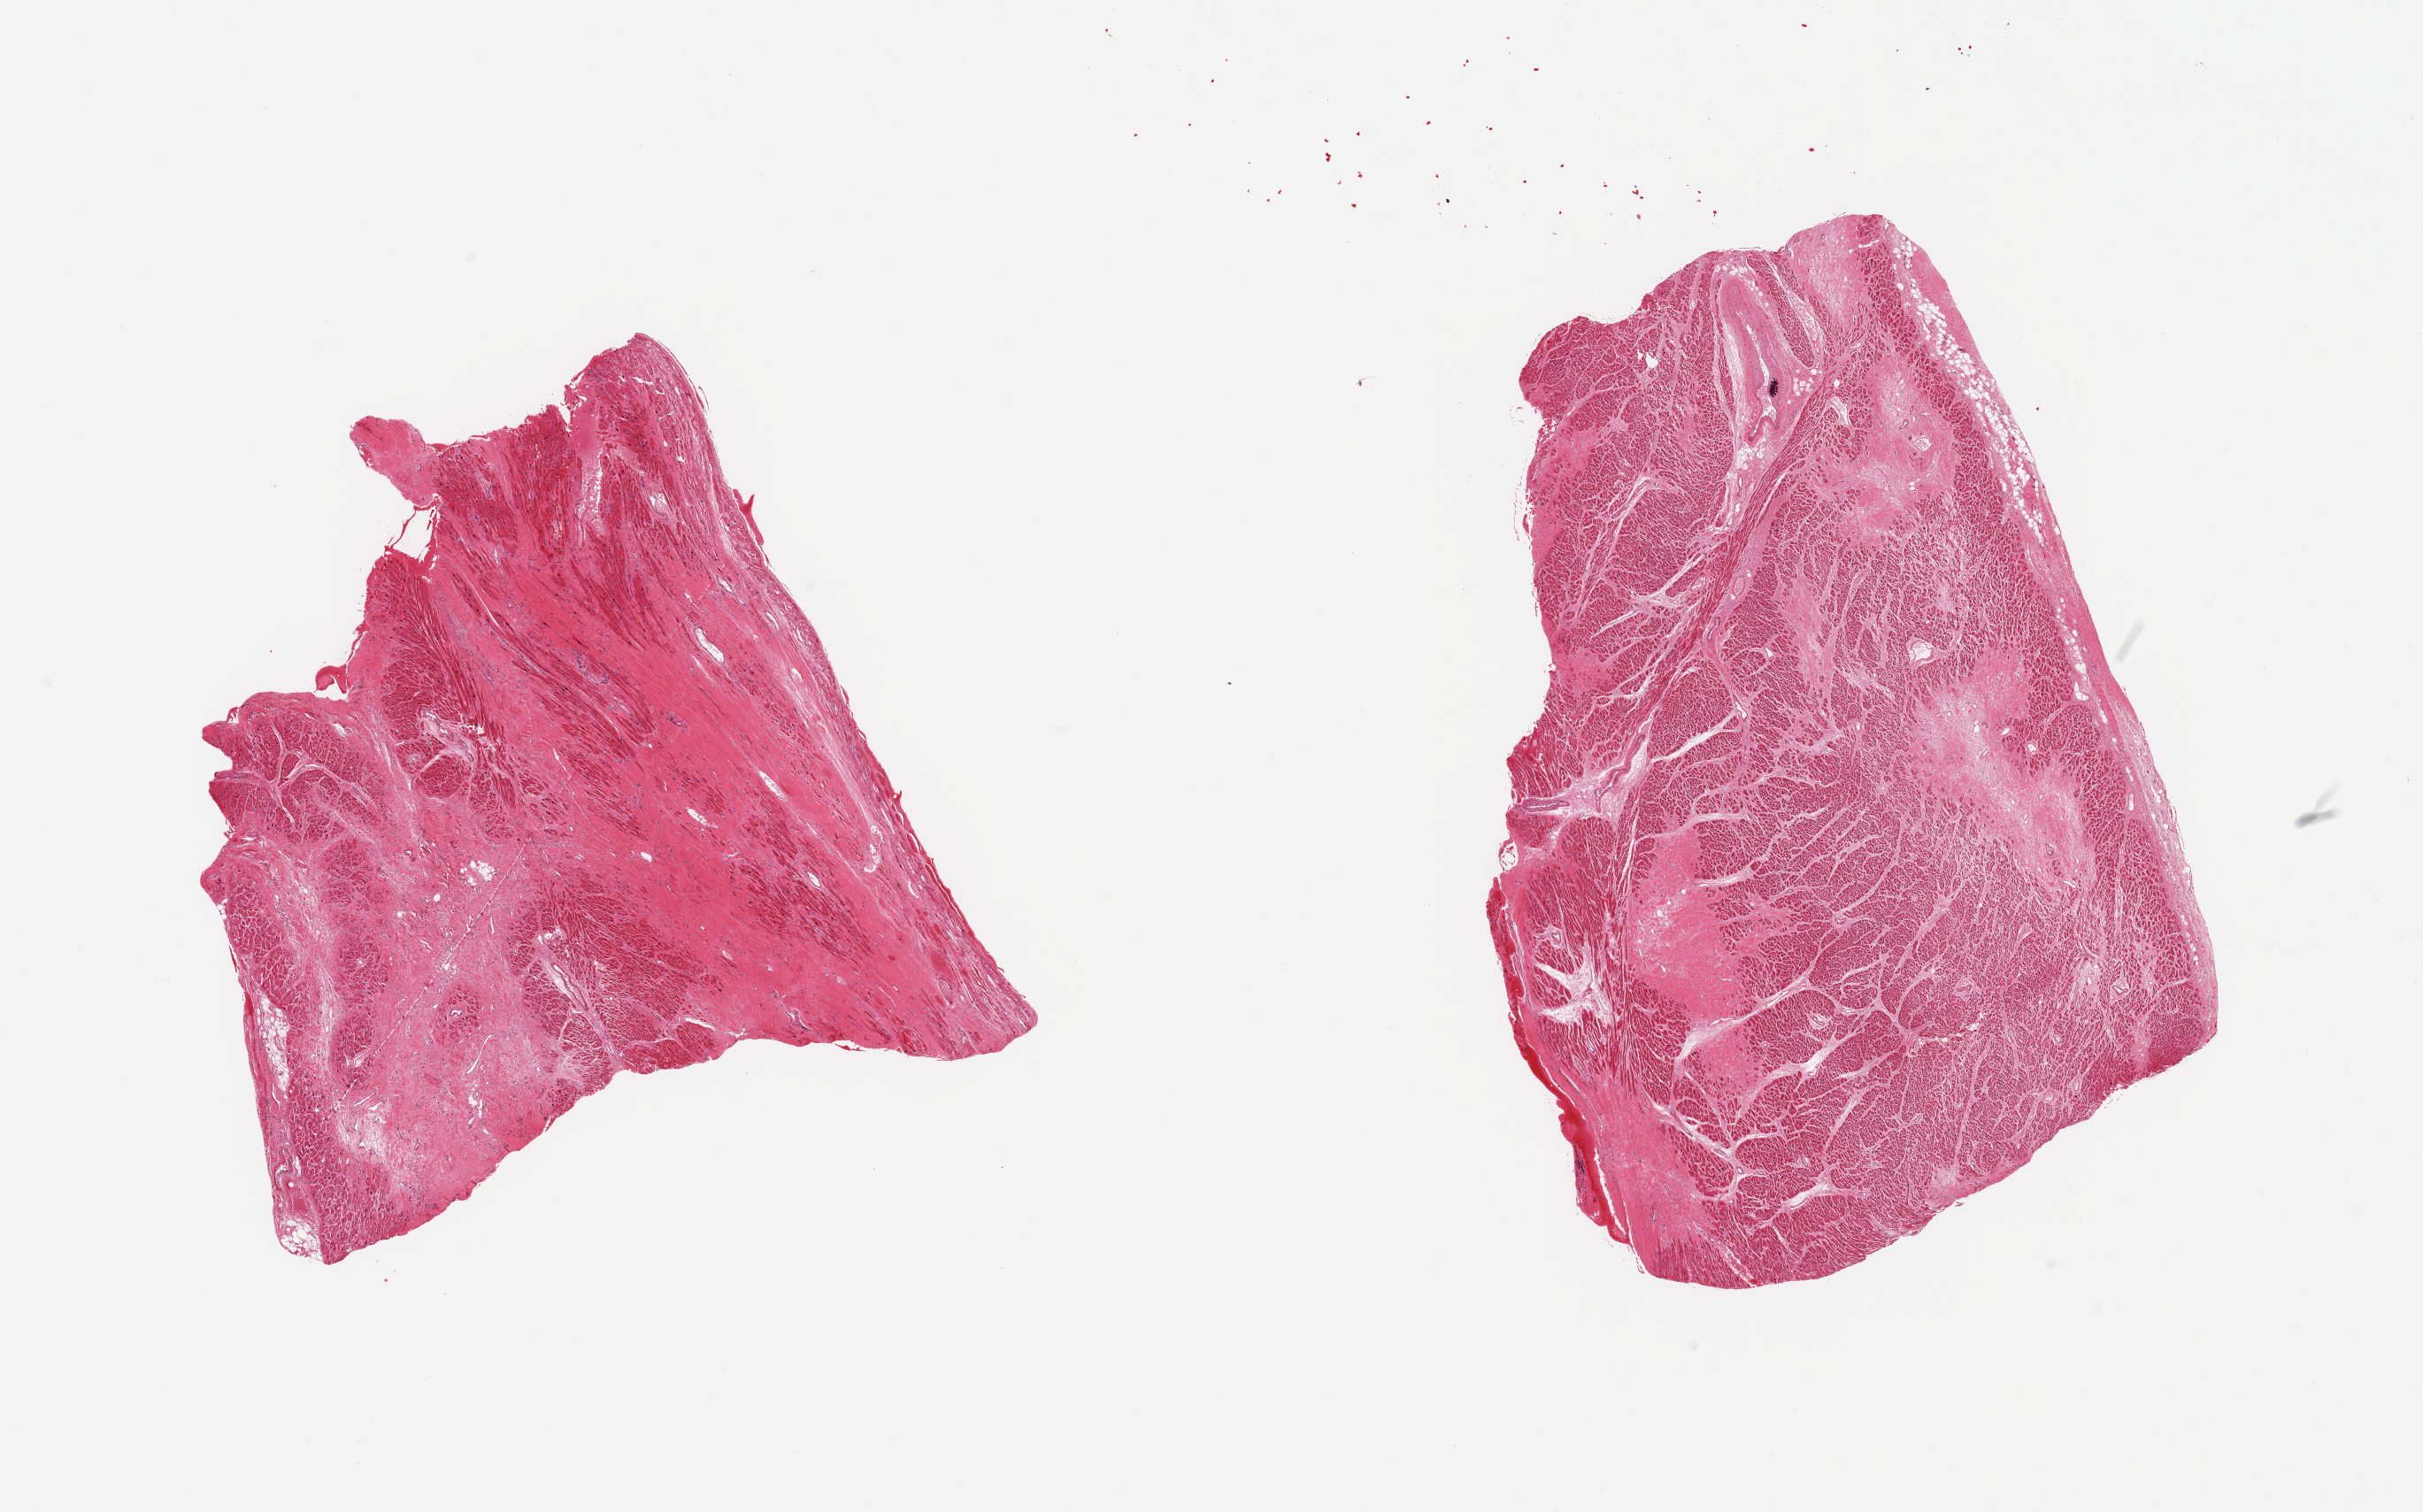
Hematoxylin and eosin (H&E) whole-slide image, brightfield, a low-resolution overview of the entire scanned area, about 21.7 x 13.5 mm; PAXgene-fixed paraffin-embedded (PFPE) section; target tissue: heart; tissue donor sample. Donor: male.
Review note (as recorded): 2 pieces; extensive scarring consistent with healed infarcts: 1 piece has 80% scar other has 30%.